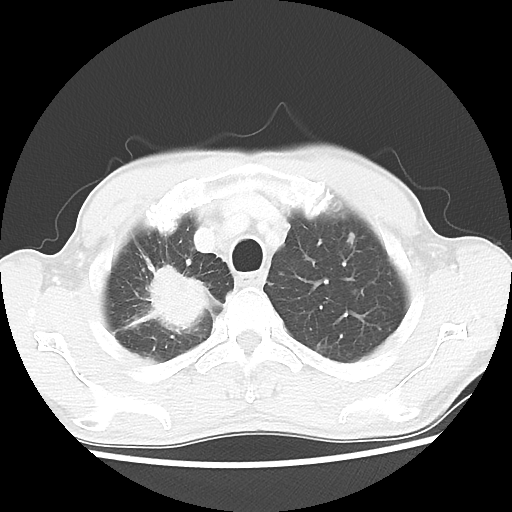
Chest CT, one axial slice; position 44 of 52 along the scan axis; 100 kVp; lung window (W 1500 / L -600 HU); 5 mm slice thickness; 512 × 512 image matrix, field of view 323 × 323 mm. Patient: male, 66 years. From the clinical record (not read from this slice): clinical TNM (as recorded): T2 N0 M1a.
Annotated regions visible in this slice (bounding box drawn by a radiologist):
- lung tumour (recorded histology: adenocarcinoma): box from (x=130, y=263) to (x=219, y=338) px